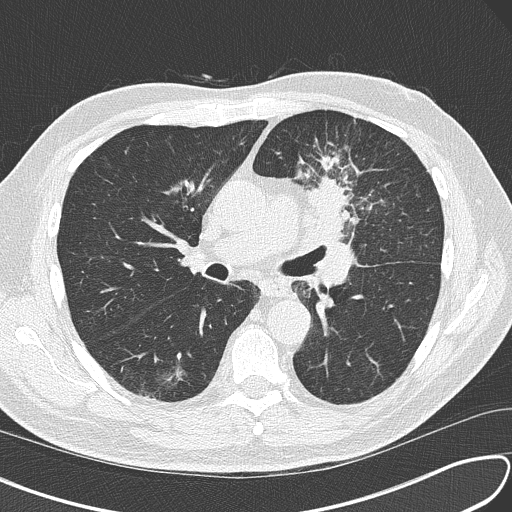
Chest CT (low-dose screening protocol), one axial image, third annual screen, lung window (W 1500 / L -600 HU), lung (sharp) reconstruction kernel (B50f), 120 kVp, slice 67 of 156 in the series, 512 × 512 image matrix. Male, age 67 years at enrolment.
- Lesion marked by an expert reader, bounding box <293,158,393,247> (left, top, right, bottom; pixels).
- Reader record for this screening exam (exam-level; its link to the box is not recorded): non-calcified nodule or mass ≥4 mm, left upper lobe, 30 × 23 mm, soft tissue attenuation, pre-existing on the prior screen: no.
- Official screen result: positive, other.
- Later outcome: lung cancer diagnosed 41 days after this screen — small cell carcinoma, NOS, left upper lobe, stage IV (AJCC 6th edition), 30 mm at pathology.